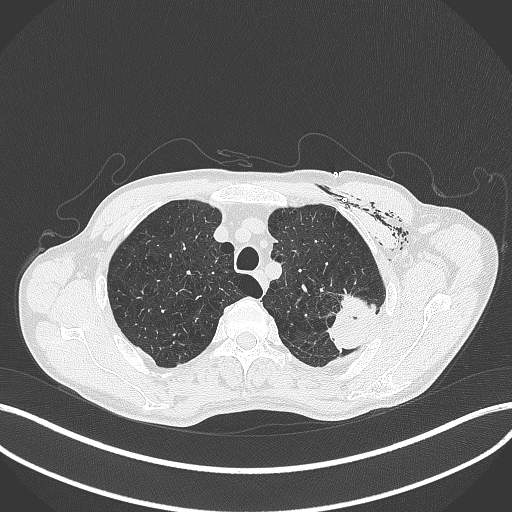
Chest CT, one axial slice. Slice 336 of 457 in the series (ordered by position). 120 kVp. Lung window (W 1500 / L -600 HU). 512 × 512 image matrix. Male patient, age 58 years. From the clinical record (not read from this slice): clinical TNM (as recorded): T3 N0 M0.
Annotated regions visible in this slice (bounding box drawn by a radiologist):
- lung tumour (recorded histology: adenocarcinoma): bounding box (x1, y1, x2, y2) in pixels: (319, 290, 384, 350)